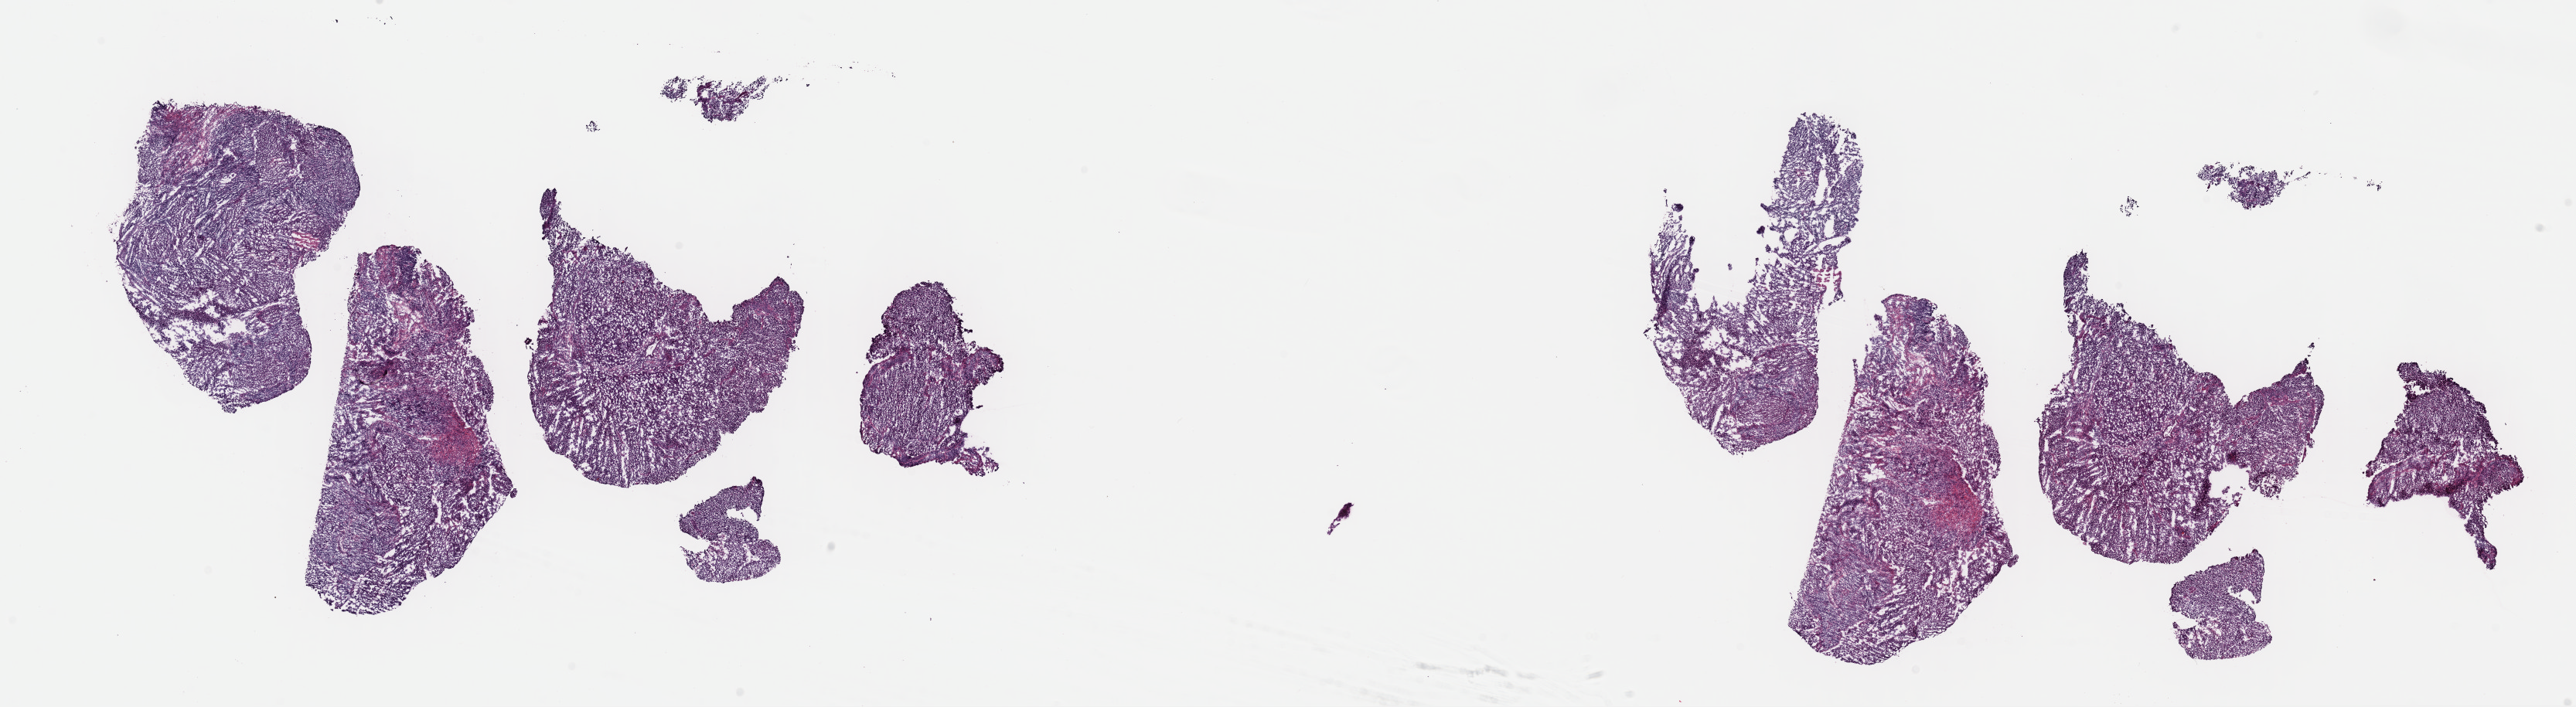
Whole-slide histology image, H&E, low-resolution overview of the scanned area, about 26.3 x 7.2 mm. Frozen section from the top of the tissue portion. Cervix, primary tumour sample. Patient: female, age at initial diagnosis 50 years. Histologic grade: G3 (poorly differentiated). Pathologist review of this section (percent, as recorded): tumour cells 80%, tumour nuclei 80%, normal cells 0%, stromal cells 15%, necrosis 5%. Inflammatory infiltration, as recorded: lymphocyte infiltration 60%, monocyte infiltration 10%, neutrophil infiltration 10%.
Pathologic diagnosis: Squamous cell carcinoma, large cell, nonkeratinizing, NOS (cervix uteri). FIGO stage: IIIB. Lymph nodes positive (case pathology): 1 of 23 examined.